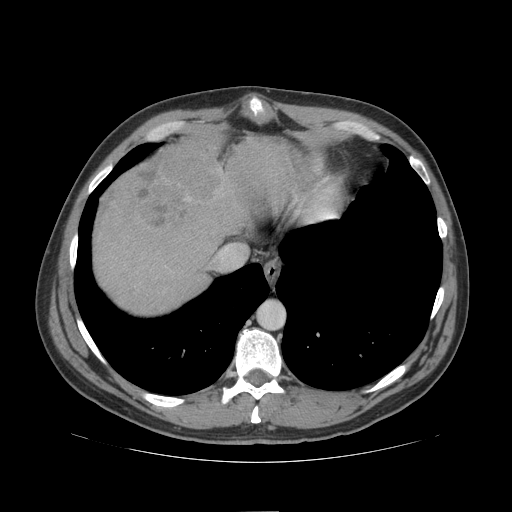
Contrast-enhanced abdominal CT (liver protocol), one axial slice. Position 89 of 109 along the scan axis. Soft-tissue window (W 400 / L 40 HU). 512 × 512 image matrix. From the clinical record (not read from this slice): diagnosis: hepatocellular carcinoma (patient treated with transarterial chemoembolisation; whether this scan precedes or follows treatment is not stated here); TNM stage (as recorded): Stage-IIIB.
Outlined on this slice (semi-automatically segmented with operator editing):
- liver parenchyma outside the tumour (the mass and vessels are separate outlines, so this box may not span the whole liver): box from (x=94, y=136) to (x=304, y=312) px
- mass: (x=112, y=137)–(x=221, y=227)